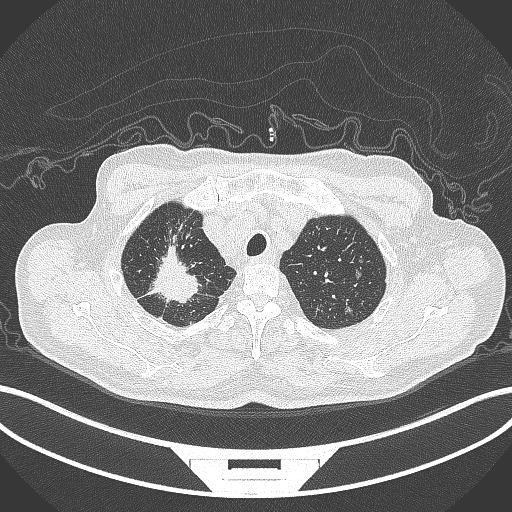
Chest CT, one axial slice. Reconstruction kernel B70f. 120 kVp. Lung window (W 1500 / L -600 HU). 1 mm slice thickness. 512 × 512 image matrix, field of view 400 × 400 mm. Male patient, age 69 years. Case-level facts recorded for this patient, not image findings: clinical TNM (as recorded): T1c N1 M1.
Outlined on this slice (rectangle marked by the reading radiologist):
- lung tumour (recorded histology: adenocarcinoma): box from (x=144, y=243) to (x=205, y=303) px